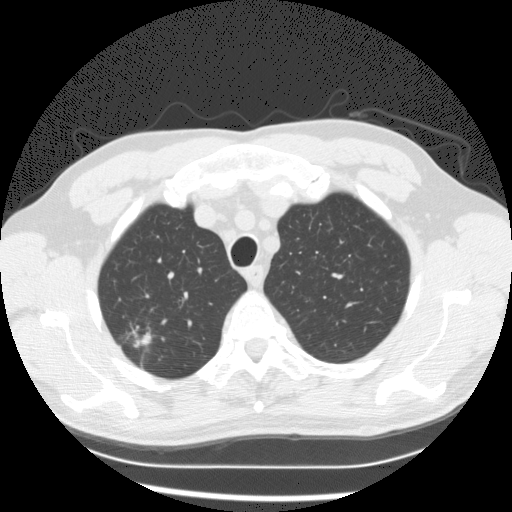
Axial slice from a low-dose chest CT screening exam, baseline annual screen, lung window (W 1500 / L -600 HU), 120 kVp. Male, age 63 years at enrolment. Current smoker at enrolment.
- Expert reader's lesion annotation, bounding box [x1, y1, x2, y2] px = [102, 307, 168, 364].
- The exam's reader record, not a measurement of the box and not confirmed to be the same lesion: non-calcified nodule or mass ≥4 mm, right upper lobe, 19 × 9 mm, poorly defined margins, mixed attenuation.
- Official screen result: positive, change unspecified: nodule(s) >= 4 mm or enlarging nodule(s), mass(es), or other non-specific abnormalities suspicious for lung cancer.